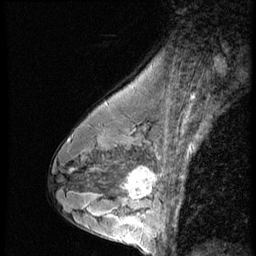
Breast MRI (dynamic contrast-enhanced), one sagittal slice. Position 36 of 56 along the scan axis. 3 images stored at this slice position (order not interpretable as contrast timing). 1.5 T. TE 4.2 ms, TR 9 ms. 256 × 256 image matrix, field of view 180 × 180 mm. Female patient, age 43 years. From the clinical record (not read from this slice): setting: breast cancer imaged before/during neoadjuvant chemotherapy; receptor status: HR-positive, HER2-negative.
Structures marked on this image (semi-automatically segmented with operator editing):
- analysis volume of interest (the breast-tissue region the enhancement analysis was run in; not a lesion): box from (x=120, y=160) to (x=163, y=207) px
- tumour enhancement mask (voxels above the 140 % enhancement threshold inside the analysis volume of interest): (x=125, y=168)–(x=158, y=199)